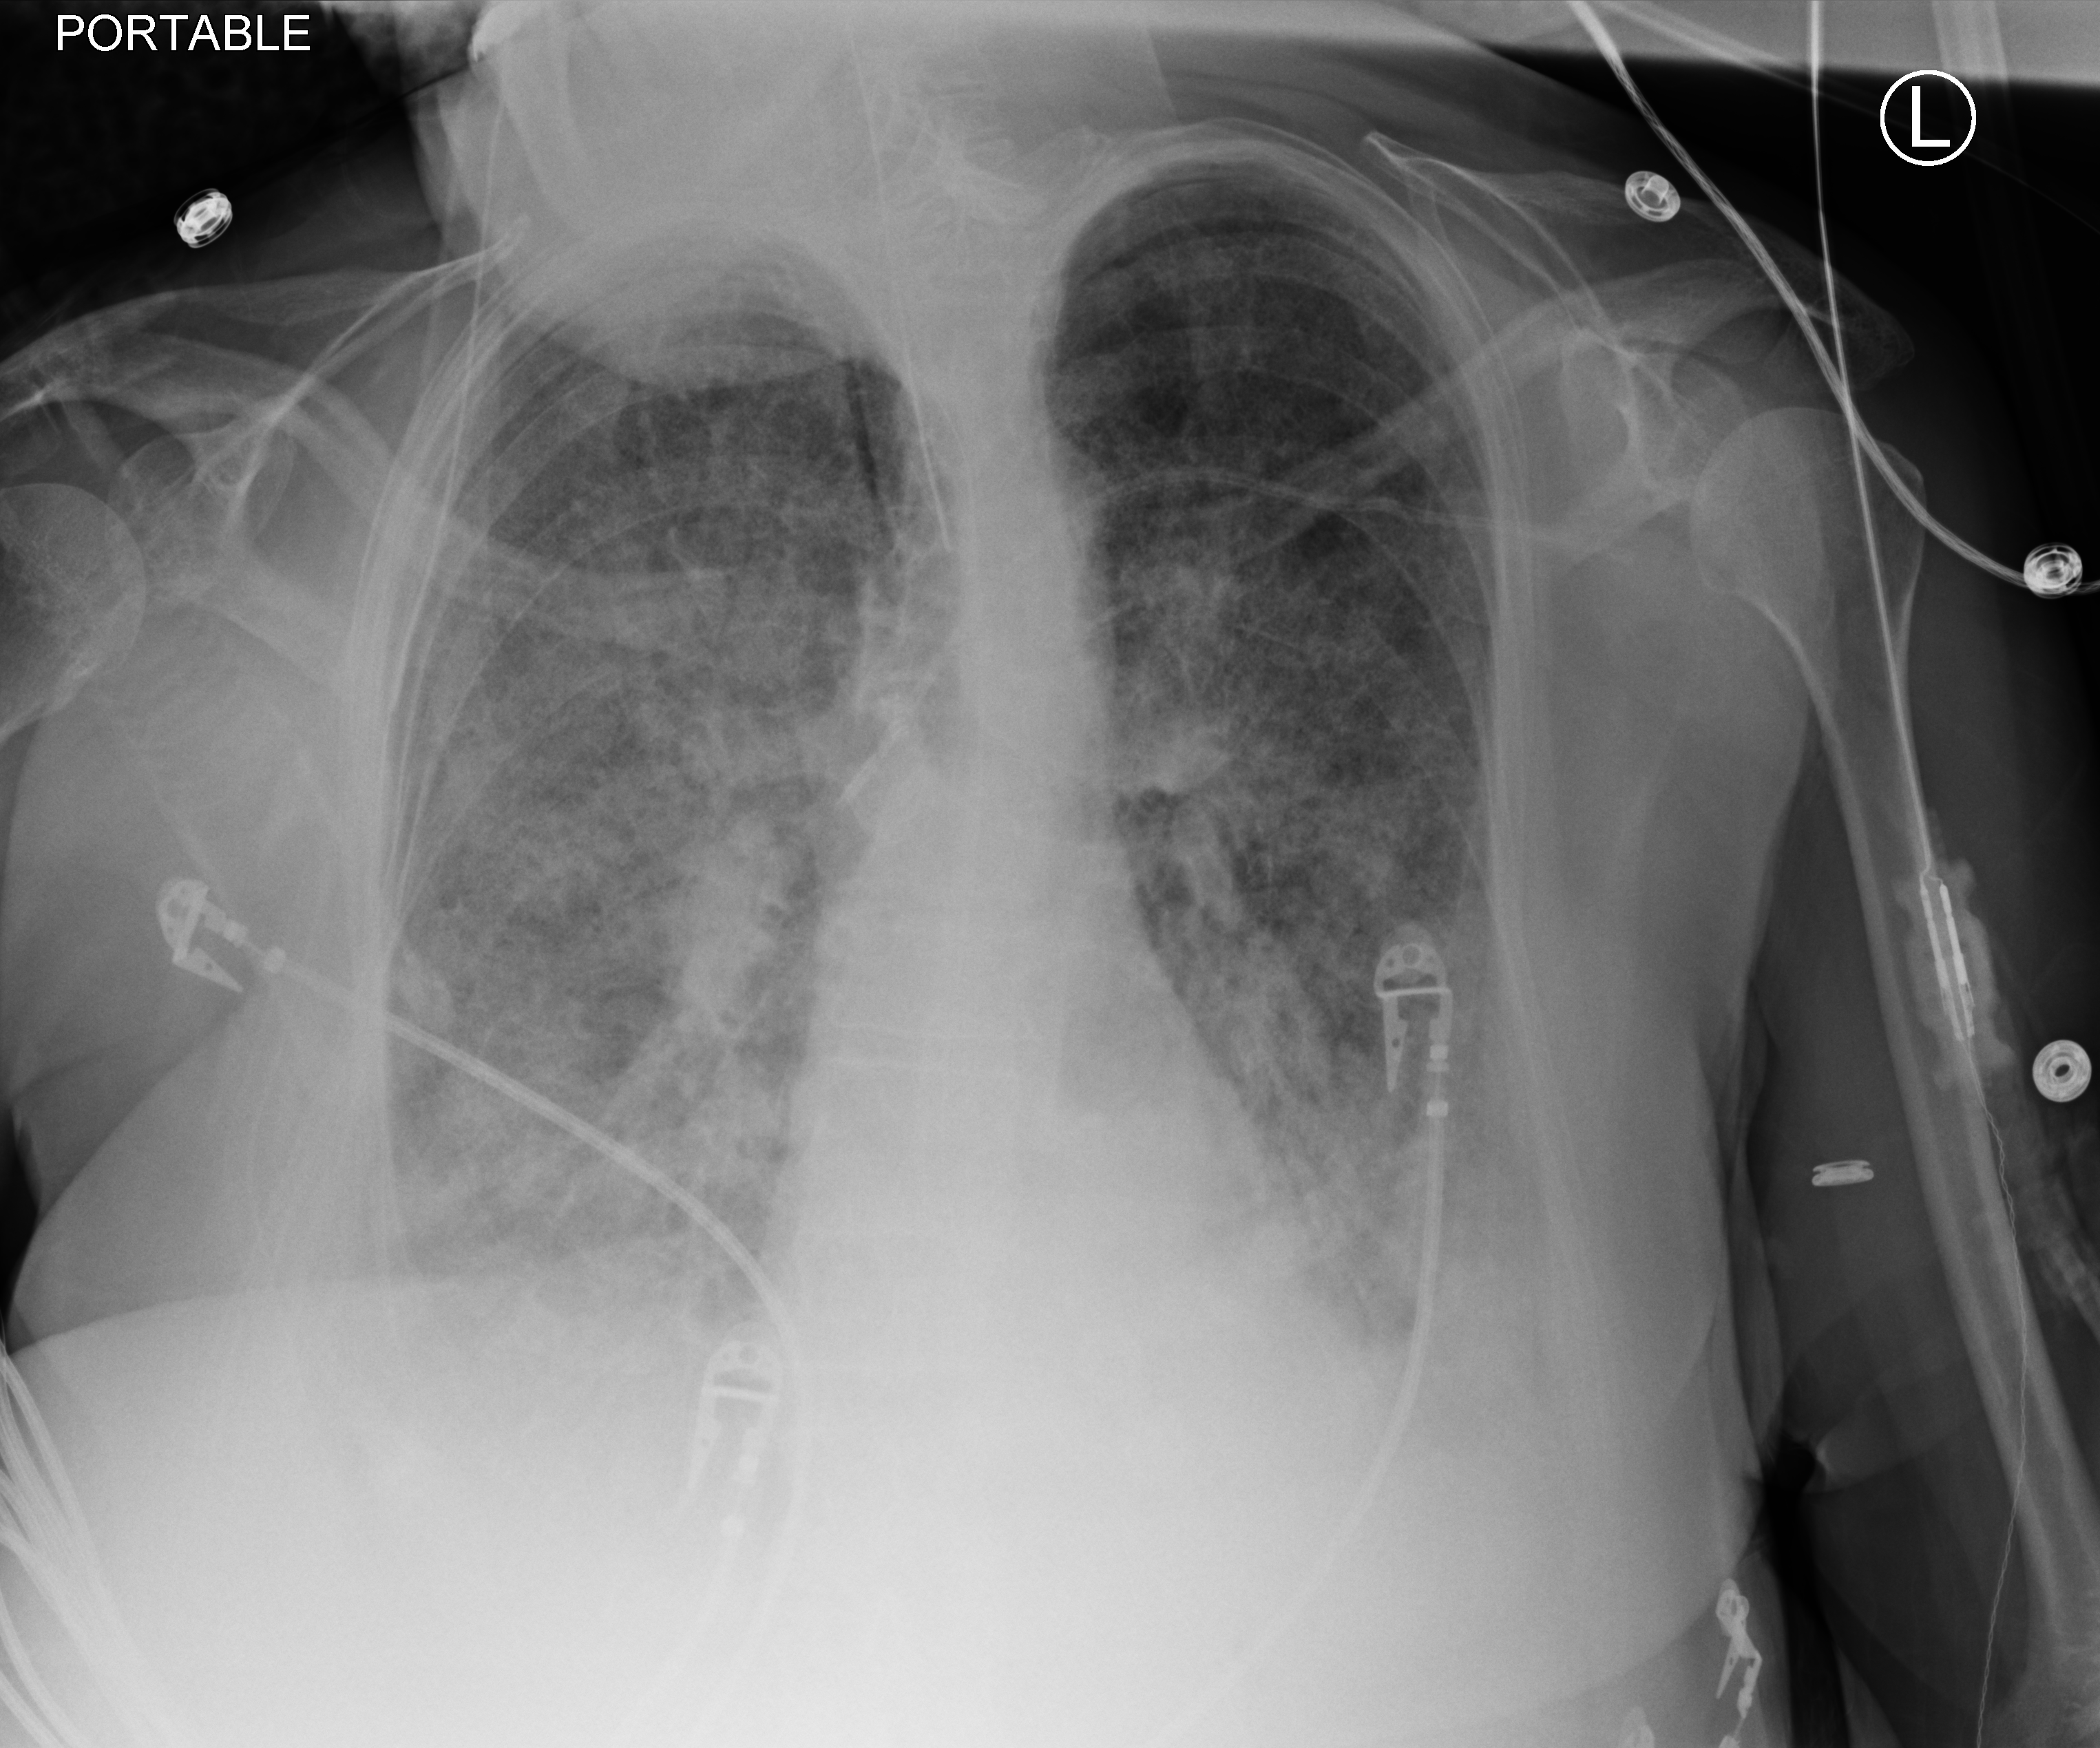
Bedside chest radiograph (computed radiography); anteroposterior (AP) projection. Patient hospitalised with COVID-19; female, aged 75–90 years.
From the hospital-stay record, not from the radiograph (when in the stay this image was taken is not recorded):
- admitted to intensive care during this hospital stay: yes
- length of hospital stay: 70 days